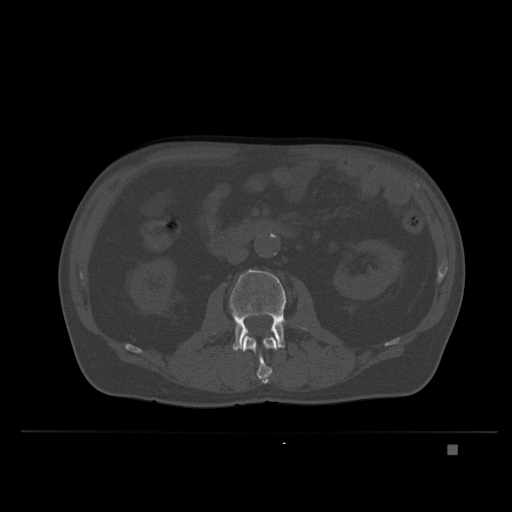
CT including the spine, one axial slice. Position 105 of 435 along the scan axis. Bone window (W 1800 / L 400 HU). 1.5 mm slice thickness. 512 × 512 image matrix. Patient: male, 73 years. Case-level facts recorded for this patient, not image findings: primary cancer: skin.
Annotated regions visible in this slice (semi-automatically segmented with operator editing):
- L2 vertebra: bounding box <242,335,279,384> (left, top, right, bottom; pixels)
- L3 vertebra: <229,269,305,351>